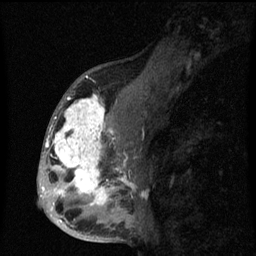
Breast MRI (dynamic contrast-enhanced), one sagittal slice. Slice 35 of 60 in the series (ordered by position). Dynamic contrast-enhanced series, image 2 of 3 at this slice position (ordered by acquisition). 1.5 T. TE 4.2 ms, TR 8 ms. 256 × 256 image matrix, field of view 190 × 190 mm. Patient: female, 50 years.
Structures marked on this image (semi-automatic segmentation, software-assisted and operator-edited):
- analysis volume of interest (the breast-tissue region the enhancement analysis was run in; not a lesion): box from (x=43, y=90) to (x=142, y=216) px
- tumour enhancement mask (voxels above the 70 % enhancement threshold inside the analysis volume of interest): (x=43, y=94)–(x=135, y=216)